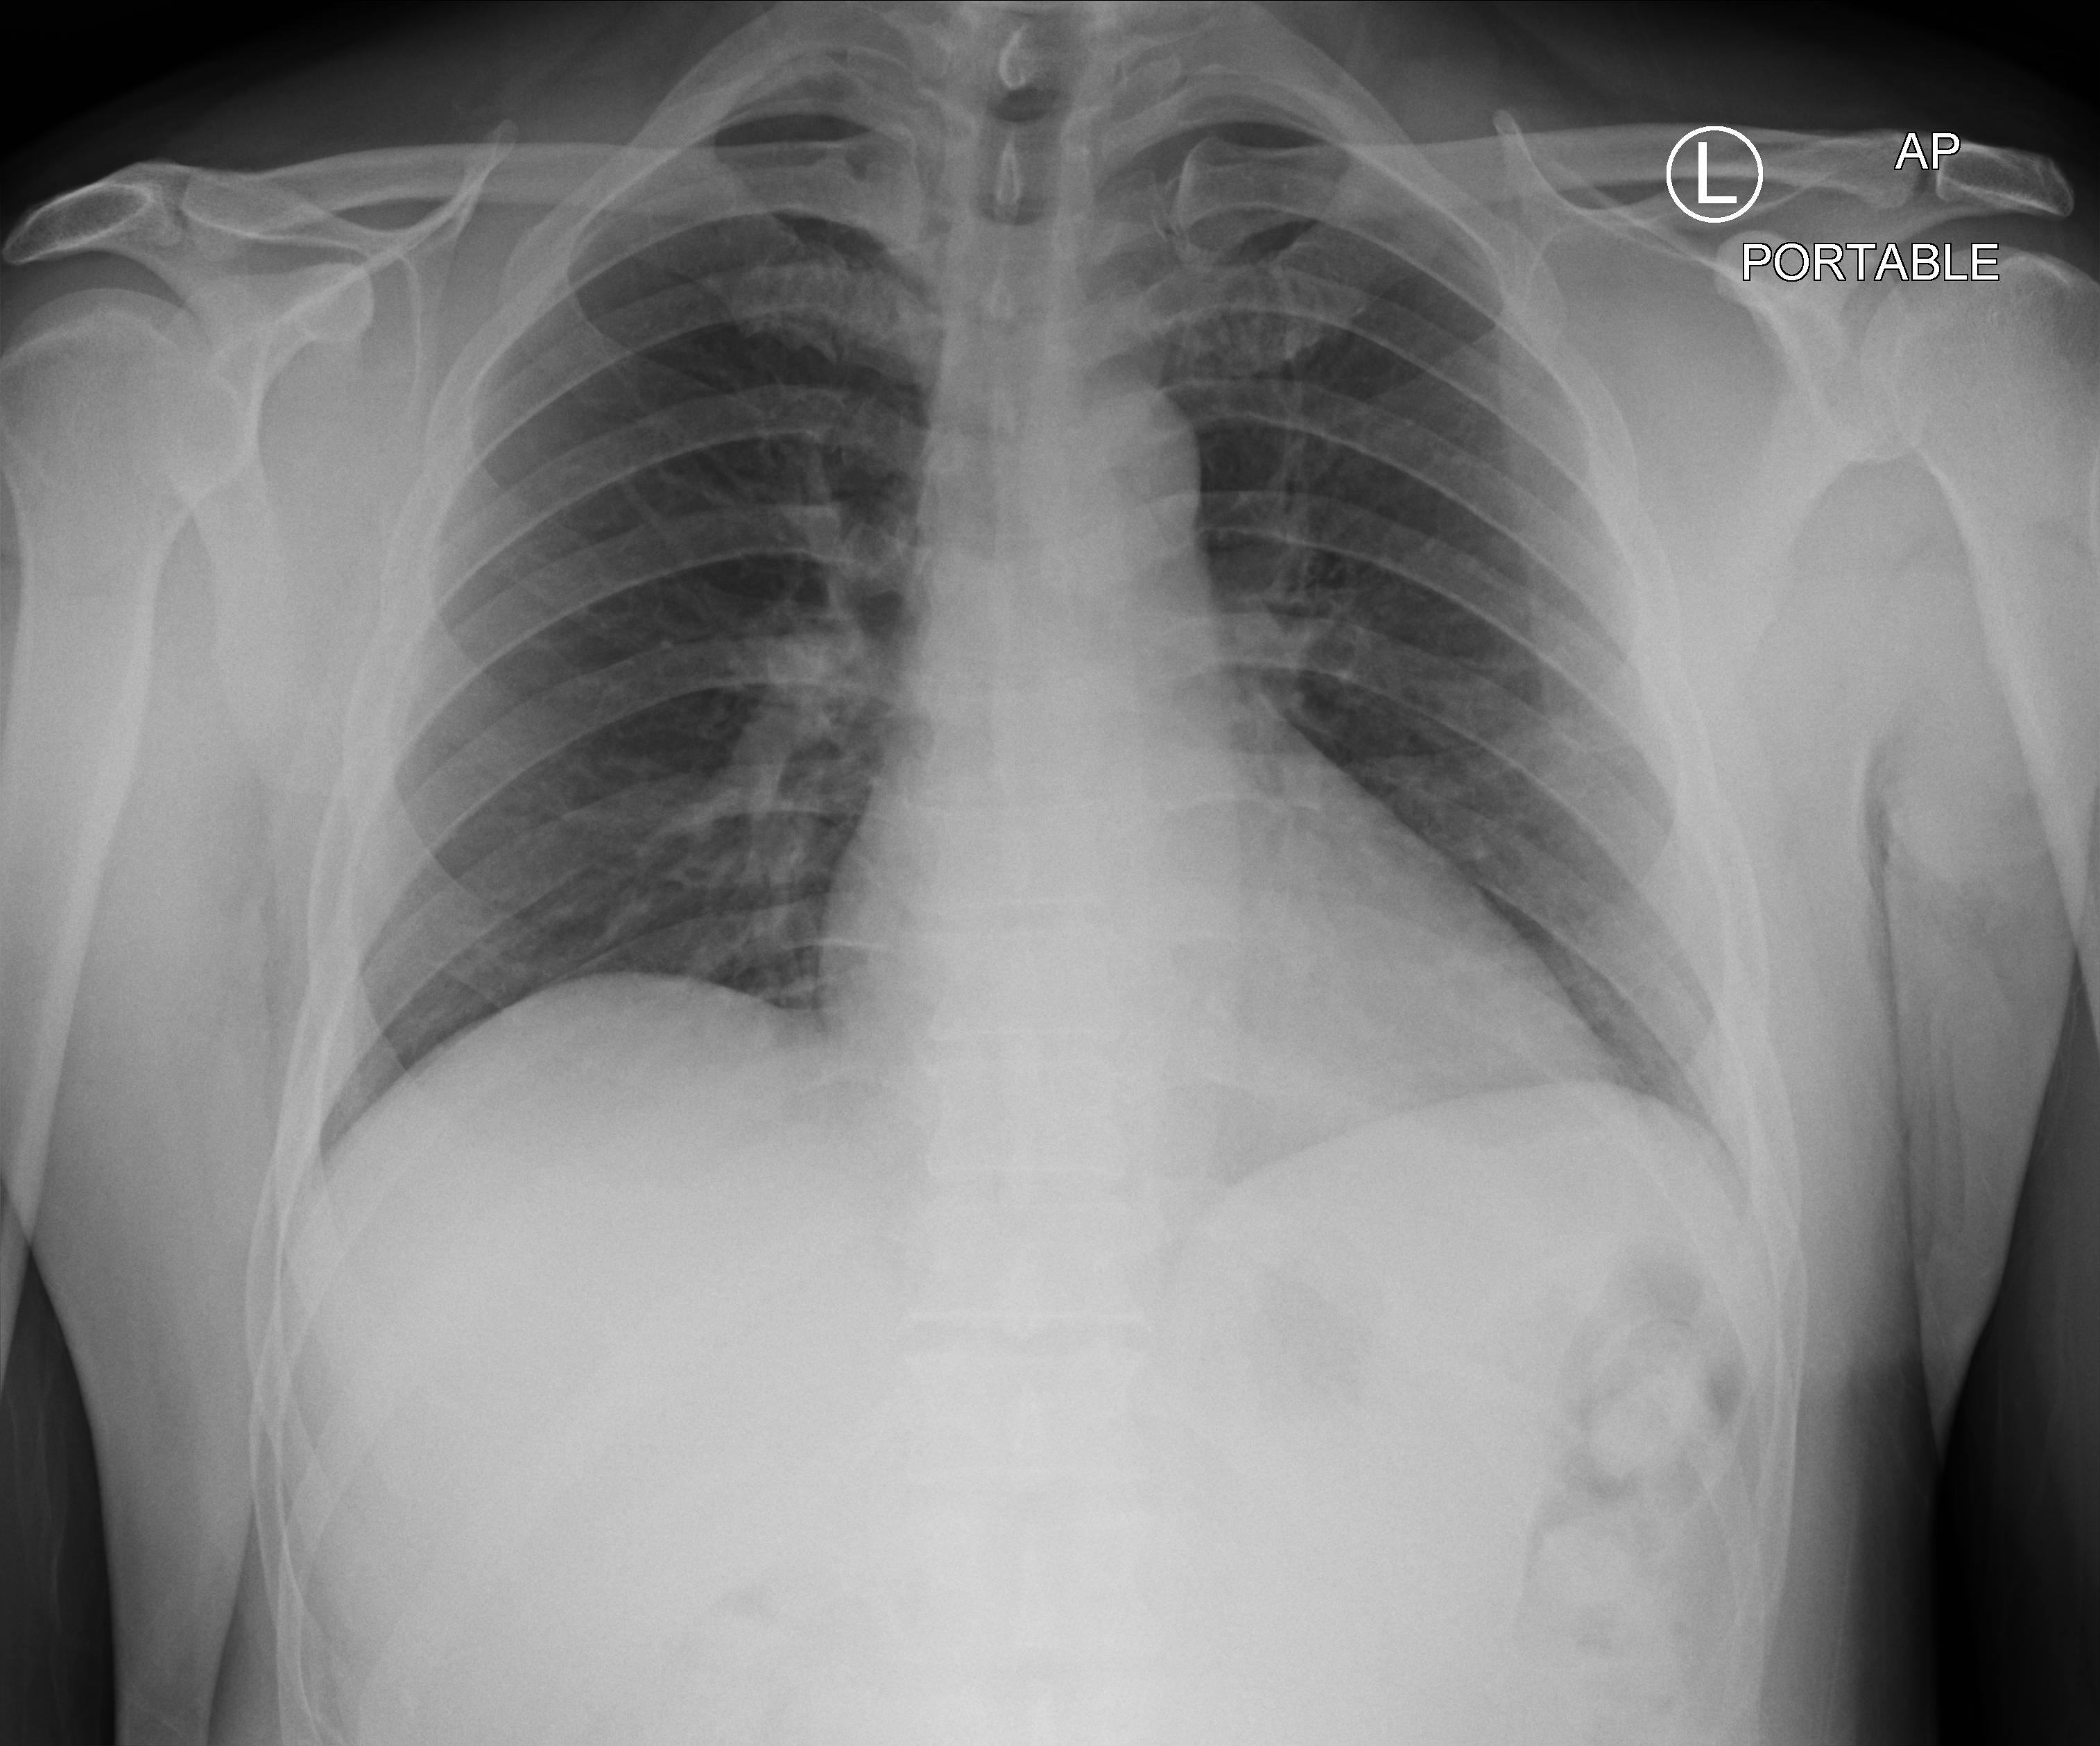
Chest X-ray (portable), anteroposterior (AP) projection. Patient hospitalised with COVID-19; male, aged 18–59 years.
Admission-level facts for this patient (not findings on this image; timing relative to this image not recorded): COPD (admission record): no; admitted to intensive care during this hospital stay: no.